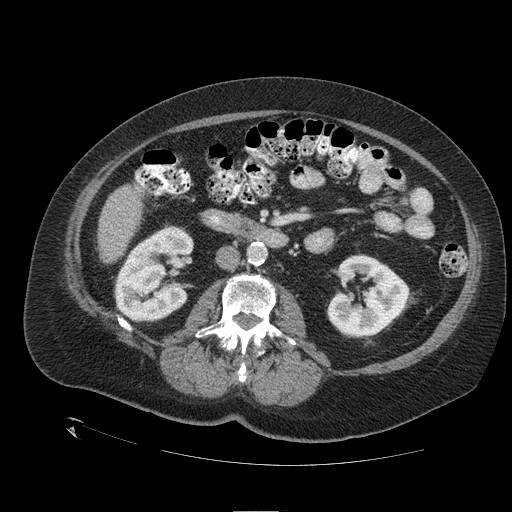
Contrast-enhanced abdominal CT (liver protocol), one axial slice; position 37 of 109 along the scan axis; reconstruction kernel STANDARD; 120 kVp; one of 2 acquisitions stored at this slice position; soft-tissue window (W 400 / L 40 HU); 2.5 mm slice thickness; 512 × 512 image matrix. From the clinical record (not read from this slice): diagnosis: hepatocellular carcinoma (patient treated with transarterial chemoembolisation; whether this scan precedes or follows treatment is not stated here); TNM stage (as recorded): Stage-I; Child-Pugh class: A; tumour size: 4.6 cm.
Outlined on this slice (semi-automatically segmented with operator editing):
- liver parenchyma outside the tumour (the mass and vessels are separate outlines, so this box may not span the whole liver): bounding box (x1, y1, x2, y2) in pixels: (98, 185, 142, 262)